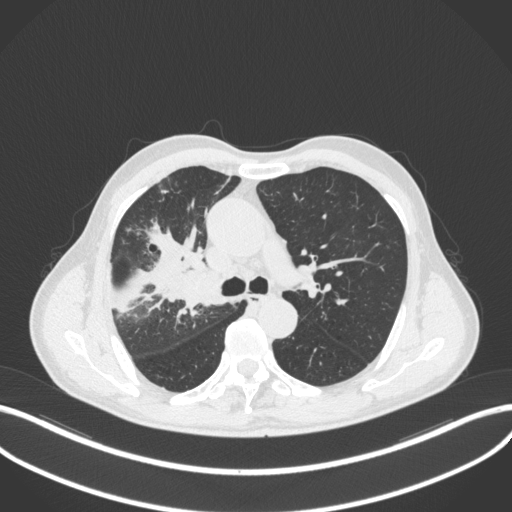
Chest CT, one axial slice; position 320 of 490 along the scan axis; reconstruction kernel B31f; lung window (W 1500 / L -600 HU); 1 mm slice thickness; 512 × 512 image matrix, field of view 400 × 400 mm. Patient: male, 69 years. Case-level facts recorded for this patient, not image findings: clinical TNM (as recorded): T2a N0 M0.
Annotated regions visible in this slice (rectangle marked by the reading radiologist):
- lung tumour (recorded histology: adenocarcinoma): box from (x=167, y=262) to (x=221, y=308) px